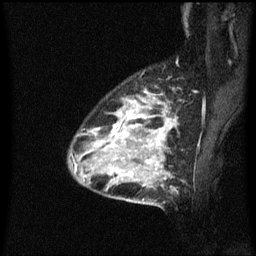
Breast MRI (dynamic contrast-enhanced), one sagittal slice. Position 46 of 60 along the scan axis. Dynamic contrast-enhanced series, image 2 of 3 at this slice position (ordered by acquisition). 1.5 T. TE 4.2 ms, TR 8.4 ms. 2 mm slice thickness. 256 × 256 image matrix. Patient: female, 34 years. From the clinical record (not read from this slice): setting: breast cancer imaged before/during neoadjuvant chemotherapy; receptor status: HR-positive, HER2-negative.
Annotated regions visible in this slice (semi-automatic segmentation, software-assisted and operator-edited):
- analysis volume of interest (the breast-tissue region the enhancement analysis was run in; not a lesion): bounding box (x1, y1, x2, y2) in pixels: (70, 92, 178, 209)
- tumour enhancement mask (voxels above the 70 % enhancement threshold inside the analysis volume of interest): (93, 100, 176, 175)